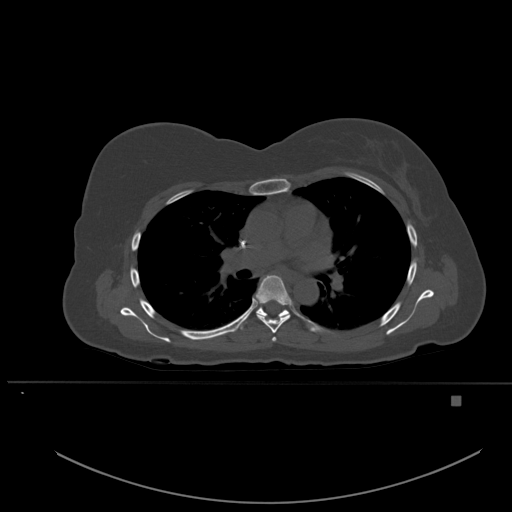
CT including the spine, one axial slice; position 360 of 651 along the scan axis; bone window (W 1800 / L 400 HU); 1.5 mm slice thickness; 512 × 512 image matrix. Patient: female, 49 years. From the clinical record (not read from this slice): primary cancer: breast; vertebrae with lytic lesions (as recorded): L3, T12, L4.
Annotated regions visible in this slice (semi-automatically segmented with operator editing):
- T4 vertebra: box from (x=272, y=337) to (x=277, y=342) px
- T5 vertebra: (x=256, y=275)–(x=291, y=333)
- T6 vertebra: (x=239, y=307)–(x=290, y=329)